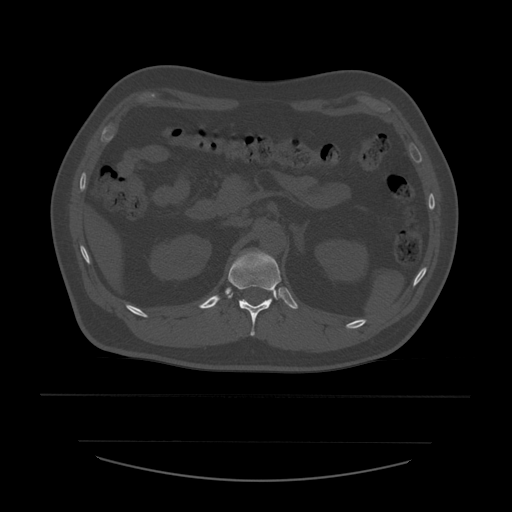
CT including the spine, one axial slice; slice 247 of 532 in the series (ordered by position); reconstruction kernel STANDARD; 120 kVp; bone window (W 1800 / L 400 HU); 1.25 mm slice thickness; 512 × 512 image matrix, field of view 441 × 441 mm. Patient age 44 years. Case-level facts recorded for this patient, not image findings: primary cancer: soft tissue sarcoma.
Outlined on this slice (semi-automatically segmented with operator editing):
- T12 vertebra: bounding box (x1, y1, x2, y2) in pixels: (228, 251, 282, 336)